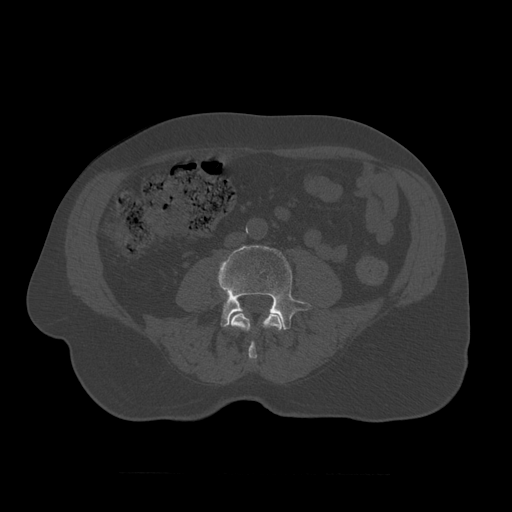
CT including the spine, one axial slice. Slice 285 of 450 in the series (ordered by position). 120 kVp. Bone window (W 1800 / L 400 HU). 1.25 mm slice thickness. 512 × 512 image matrix. Patient age 75 years. Case-level facts recorded for this patient, not image findings: primary cancer: prostate.
Outlined on this slice (semi-automatic segmentation, software-assisted and operator-edited):
- L3 vertebra: box from (x=230, y=310) to (x=284, y=360) px
- L4 vertebra: (x=218, y=246)–(x=312, y=330)